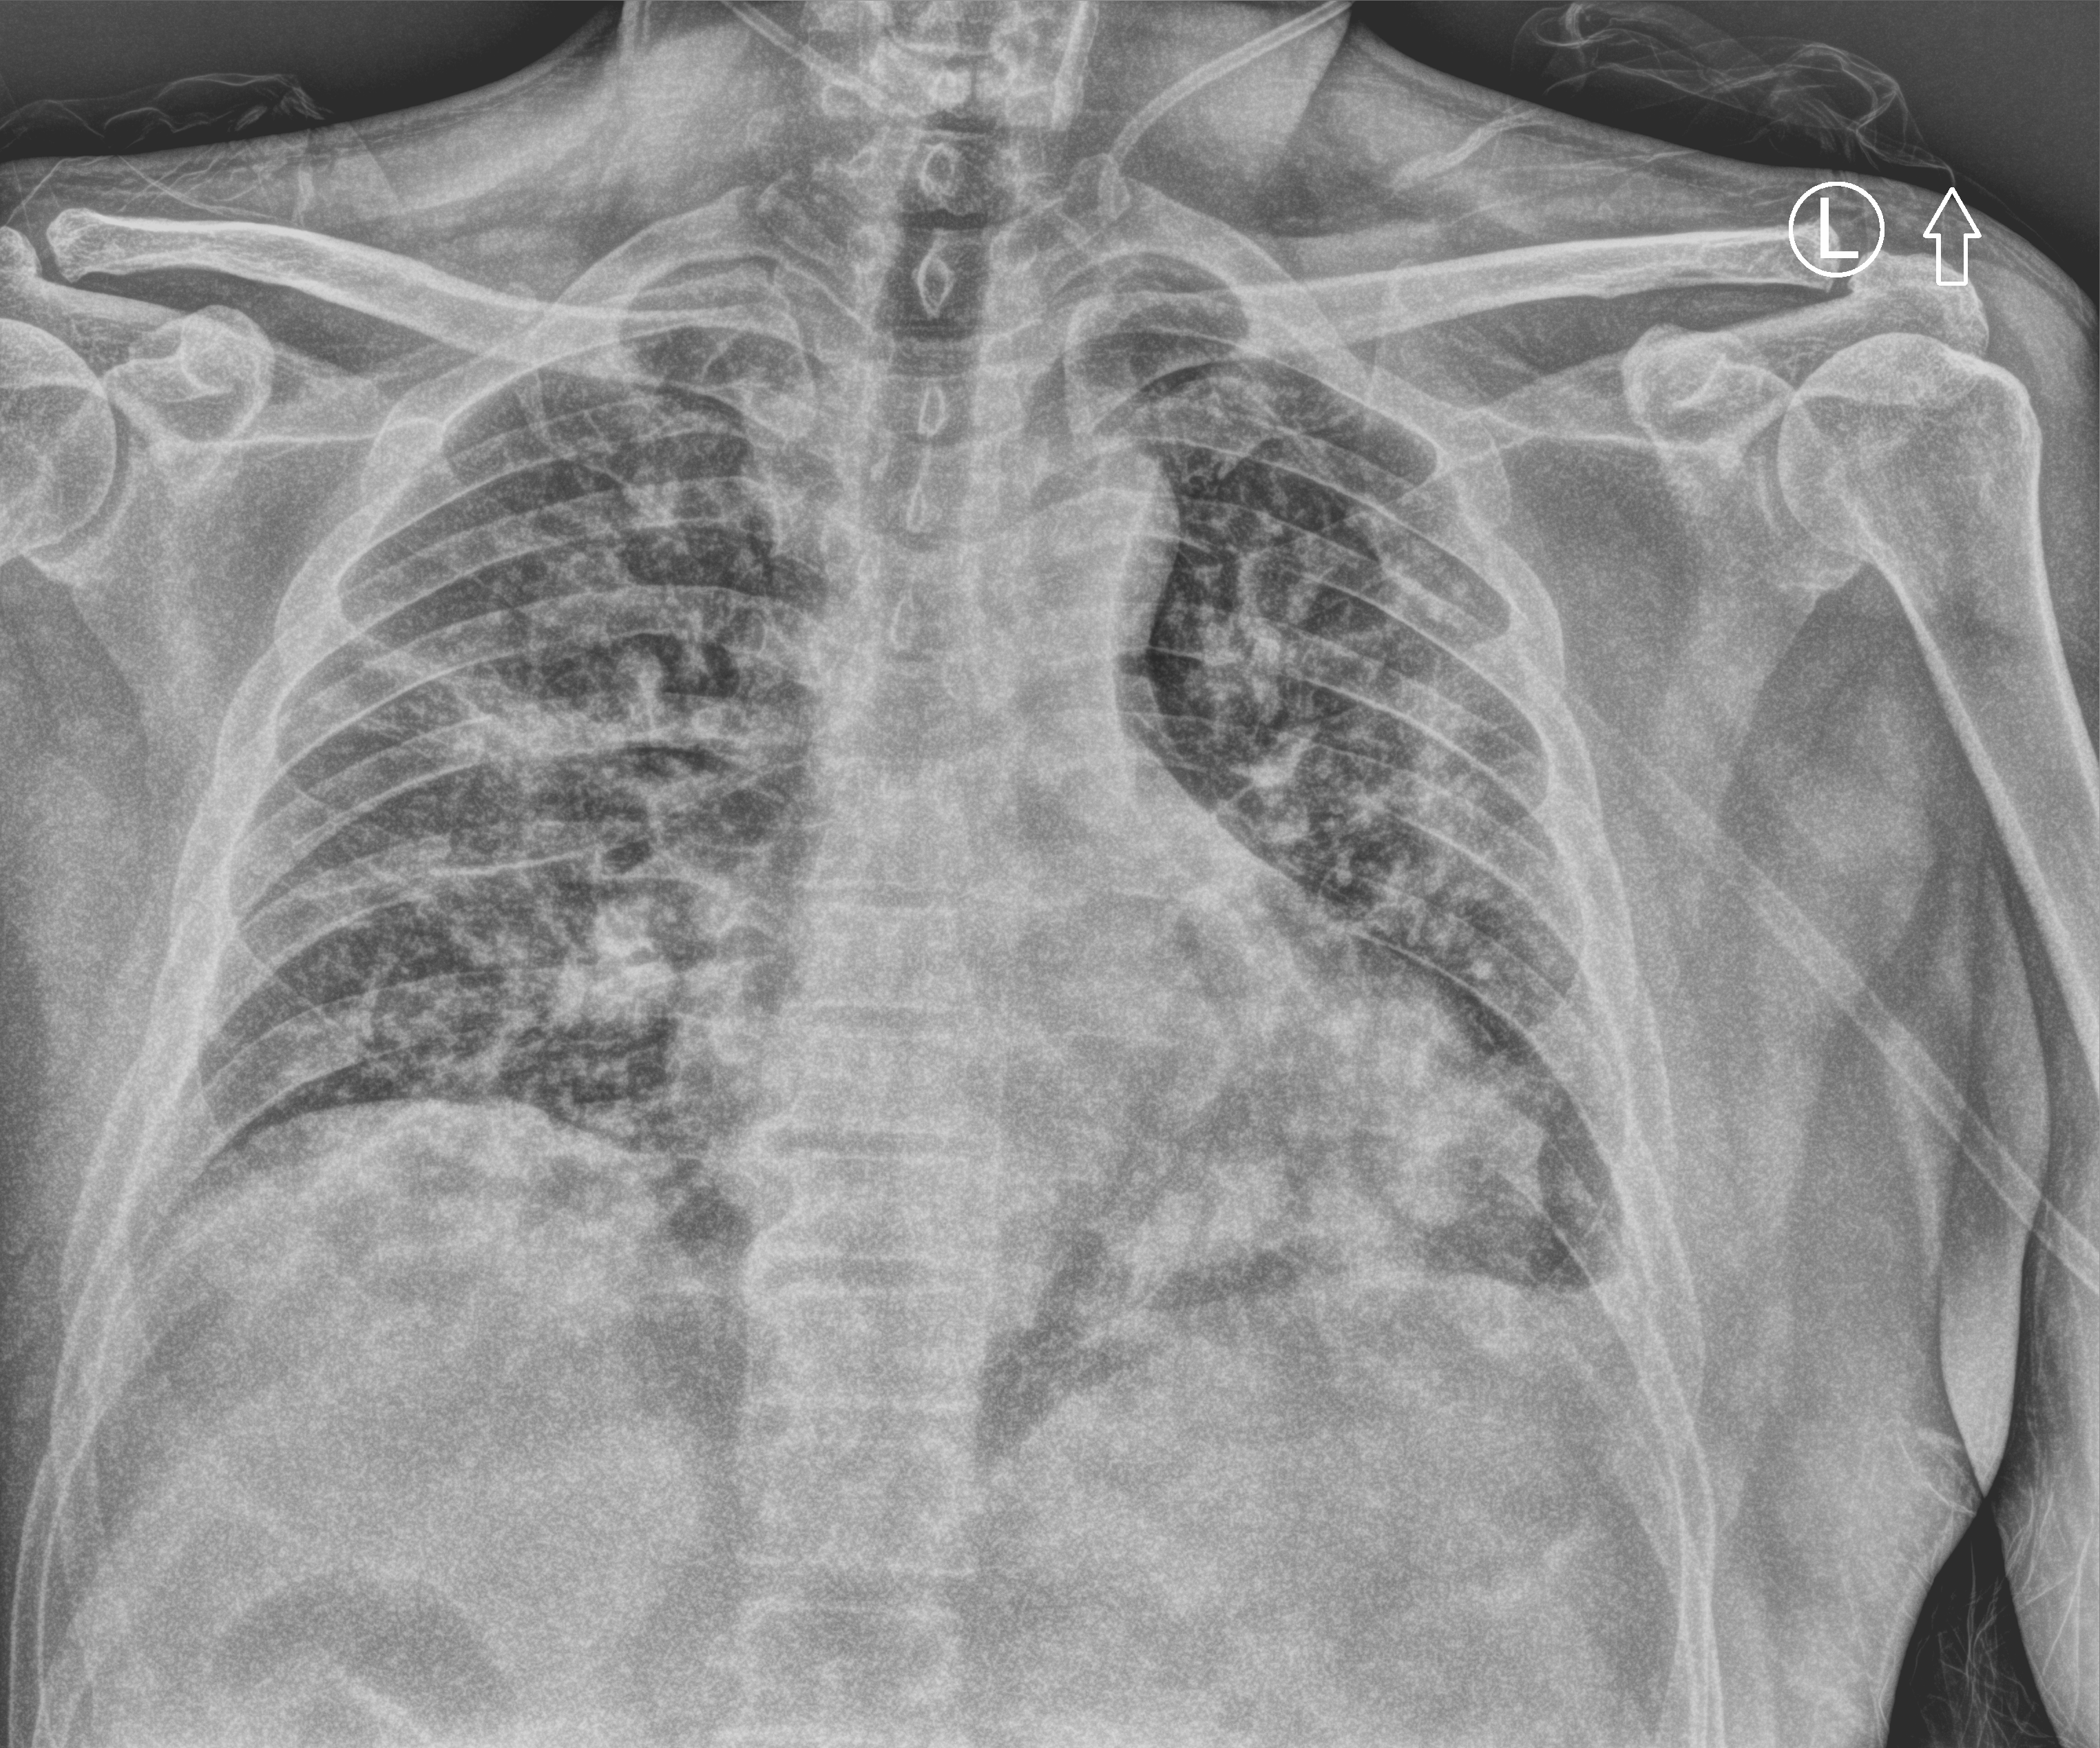
Chest X-ray (portable), anteroposterior (AP) projection. Male patient hospitalised with COVID-19, age 60–74 years.
From the hospital-stay record, not from the radiograph (when in the stay this image was taken is not recorded): other chronic lung disease (admission record): no; admitted to intensive care during this hospital stay: no.